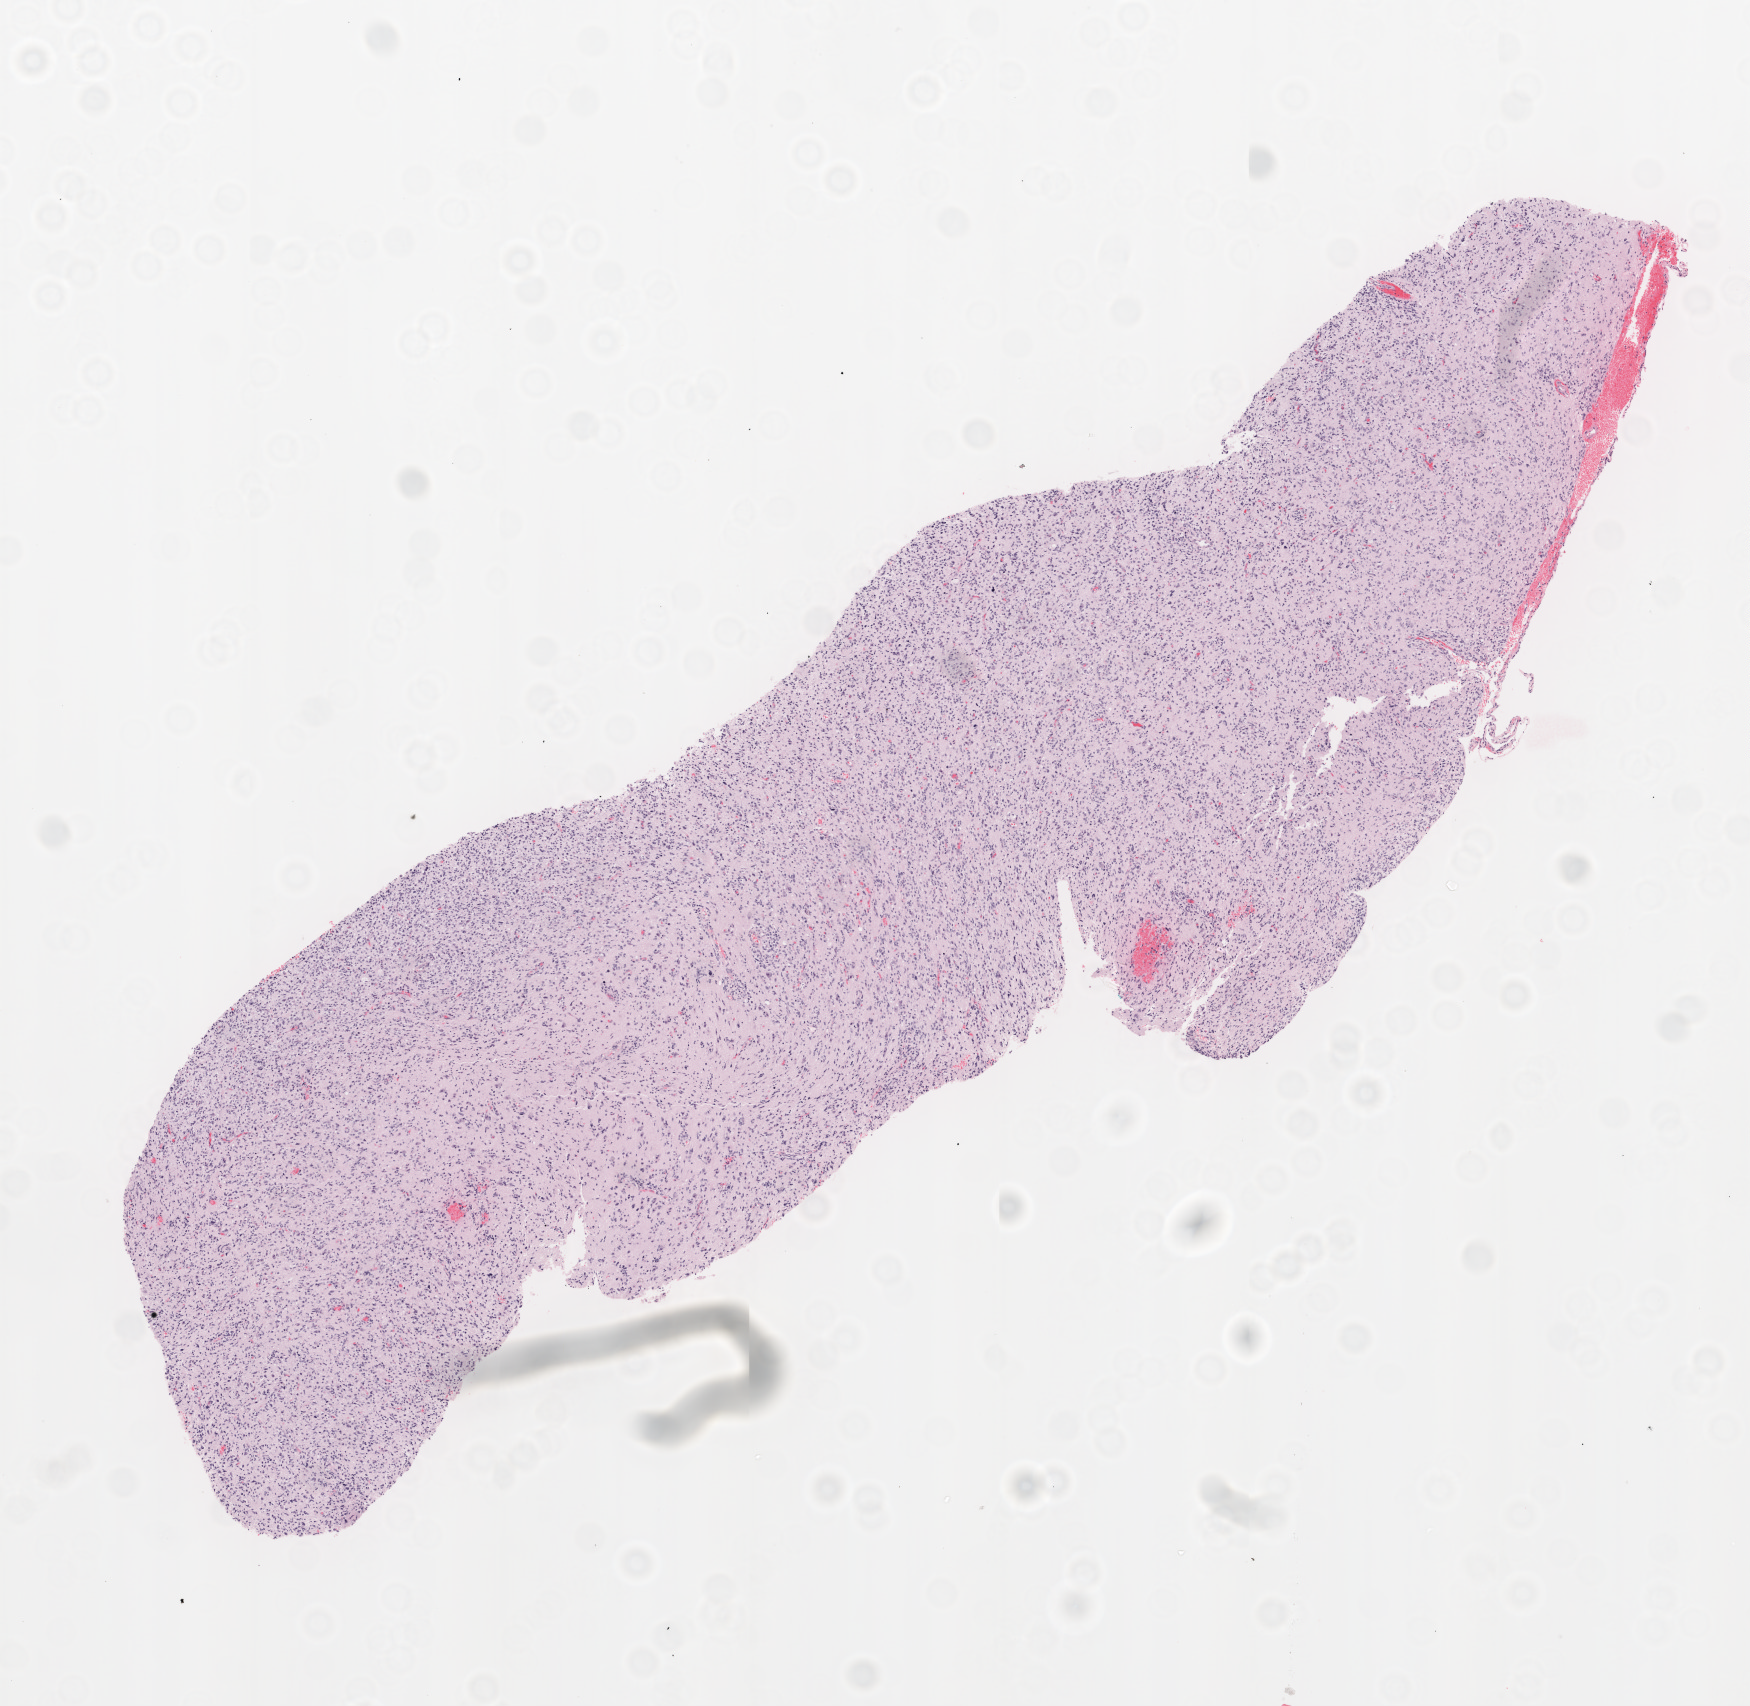
Hematoxylin and eosin (H&E) stained whole-slide image, low-resolution overview of the scanned area, about 7.0 x 6.8 mm (acquisition: 20x scan). Frozen section from the top of the tissue portion. Brain, primary tumour sample. Male, age 51 years at initial diagnosis. Slide review estimates, as recorded: tumour cells 100%, tumour nuclei 85%, normal cells 0%, stromal cells 0%, necrosis 0%.
* histologic diagnosis: Glioblastoma